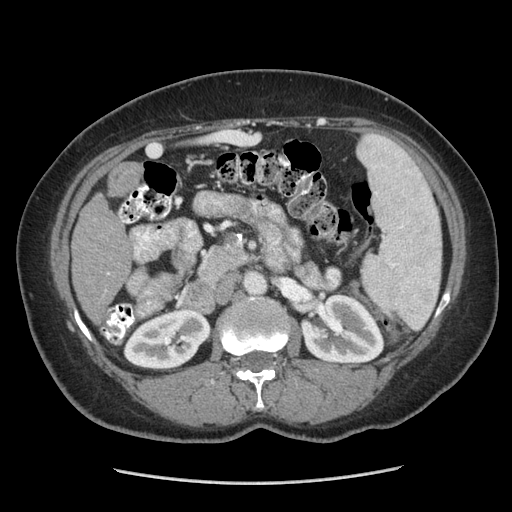
Contrast-enhanced abdominal CT (liver protocol), one axial slice. 140 kVp. Soft-tissue window (W 400 / L 40 HU). 2.5 mm slice thickness. 512 × 512 image matrix. From the clinical record (not read from this slice): diagnosis: hepatocellular carcinoma (patient treated with transarterial chemoembolisation; whether this scan precedes or follows treatment is not stated here); TNM stage (as recorded): Stage-I; Child-Pugh class: A; tumour differentiation: poorly differentiated; tumour nodularity: uninodular.
Annotated regions visible in this slice (semi-automatically segmented with operator editing):
- liver parenchyma outside the tumour (the mass and vessels are separate outlines, so this box may not span the whole liver): bounding box [x1, y1, x2, y2] px = [72, 194, 132, 304]
- mass: [109, 163, 141, 195]